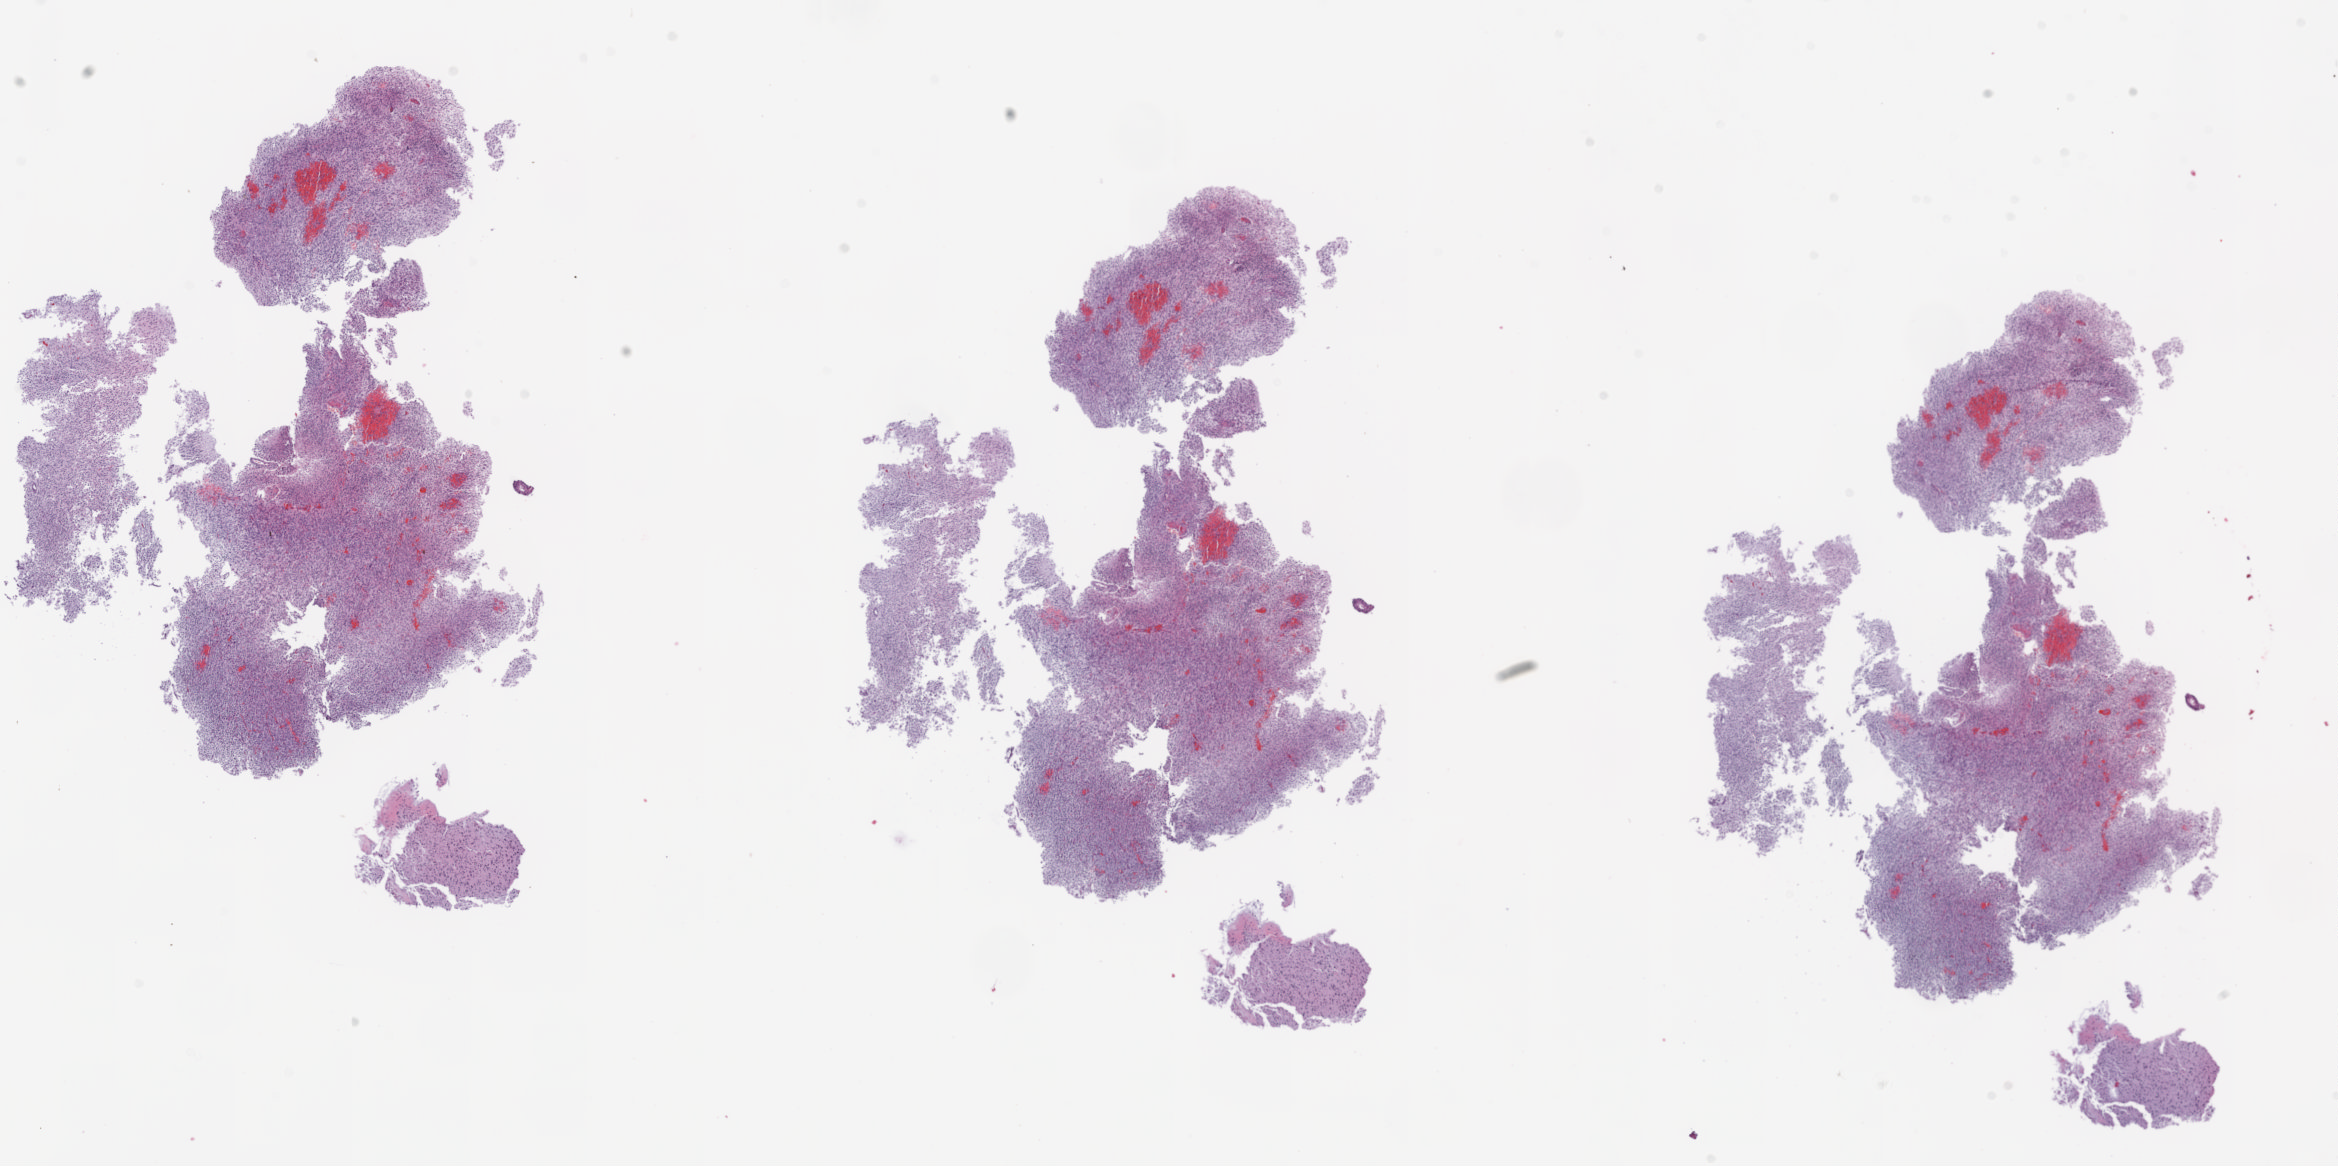
Whole-slide histology image, H&E, a low-resolution overview of the entire scanned area, about 18.7 x 9.3 mm (acquisition: 5x scan). Frozen section from the top of the tissue portion. Sample: primary tumour, brain. Patient: female, age at initial diagnosis 75 years. Slide review estimates, as recorded: tumour cells 100%, tumour nuclei 85%, normal cells 0%, stromal cells 0%, necrosis 0%.
Pathologic diagnosis: Glioblastoma.